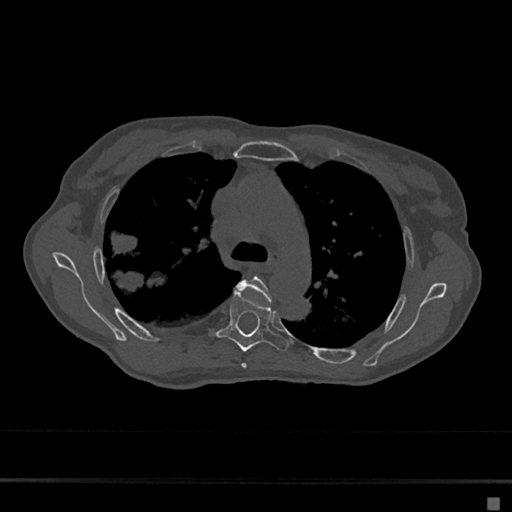
CT including the spine, one axial slice; slice 469 of 797 in the series (ordered by position); 120 kVp; bone window (W 1800 / L 400 HU); 0.5 mm slice thickness; 512 × 512 image matrix. Patient: female, 68 years. Case-level facts recorded for this patient, not image findings: primary cancer: renal.
Outlined on this slice (semi-automatic segmentation, software-assisted and operator-edited):
- T4 vertebra: bounding box <236,276,272,369> (left, top, right, bottom; pixels)
- T5 vertebra: <210,291,288,352>